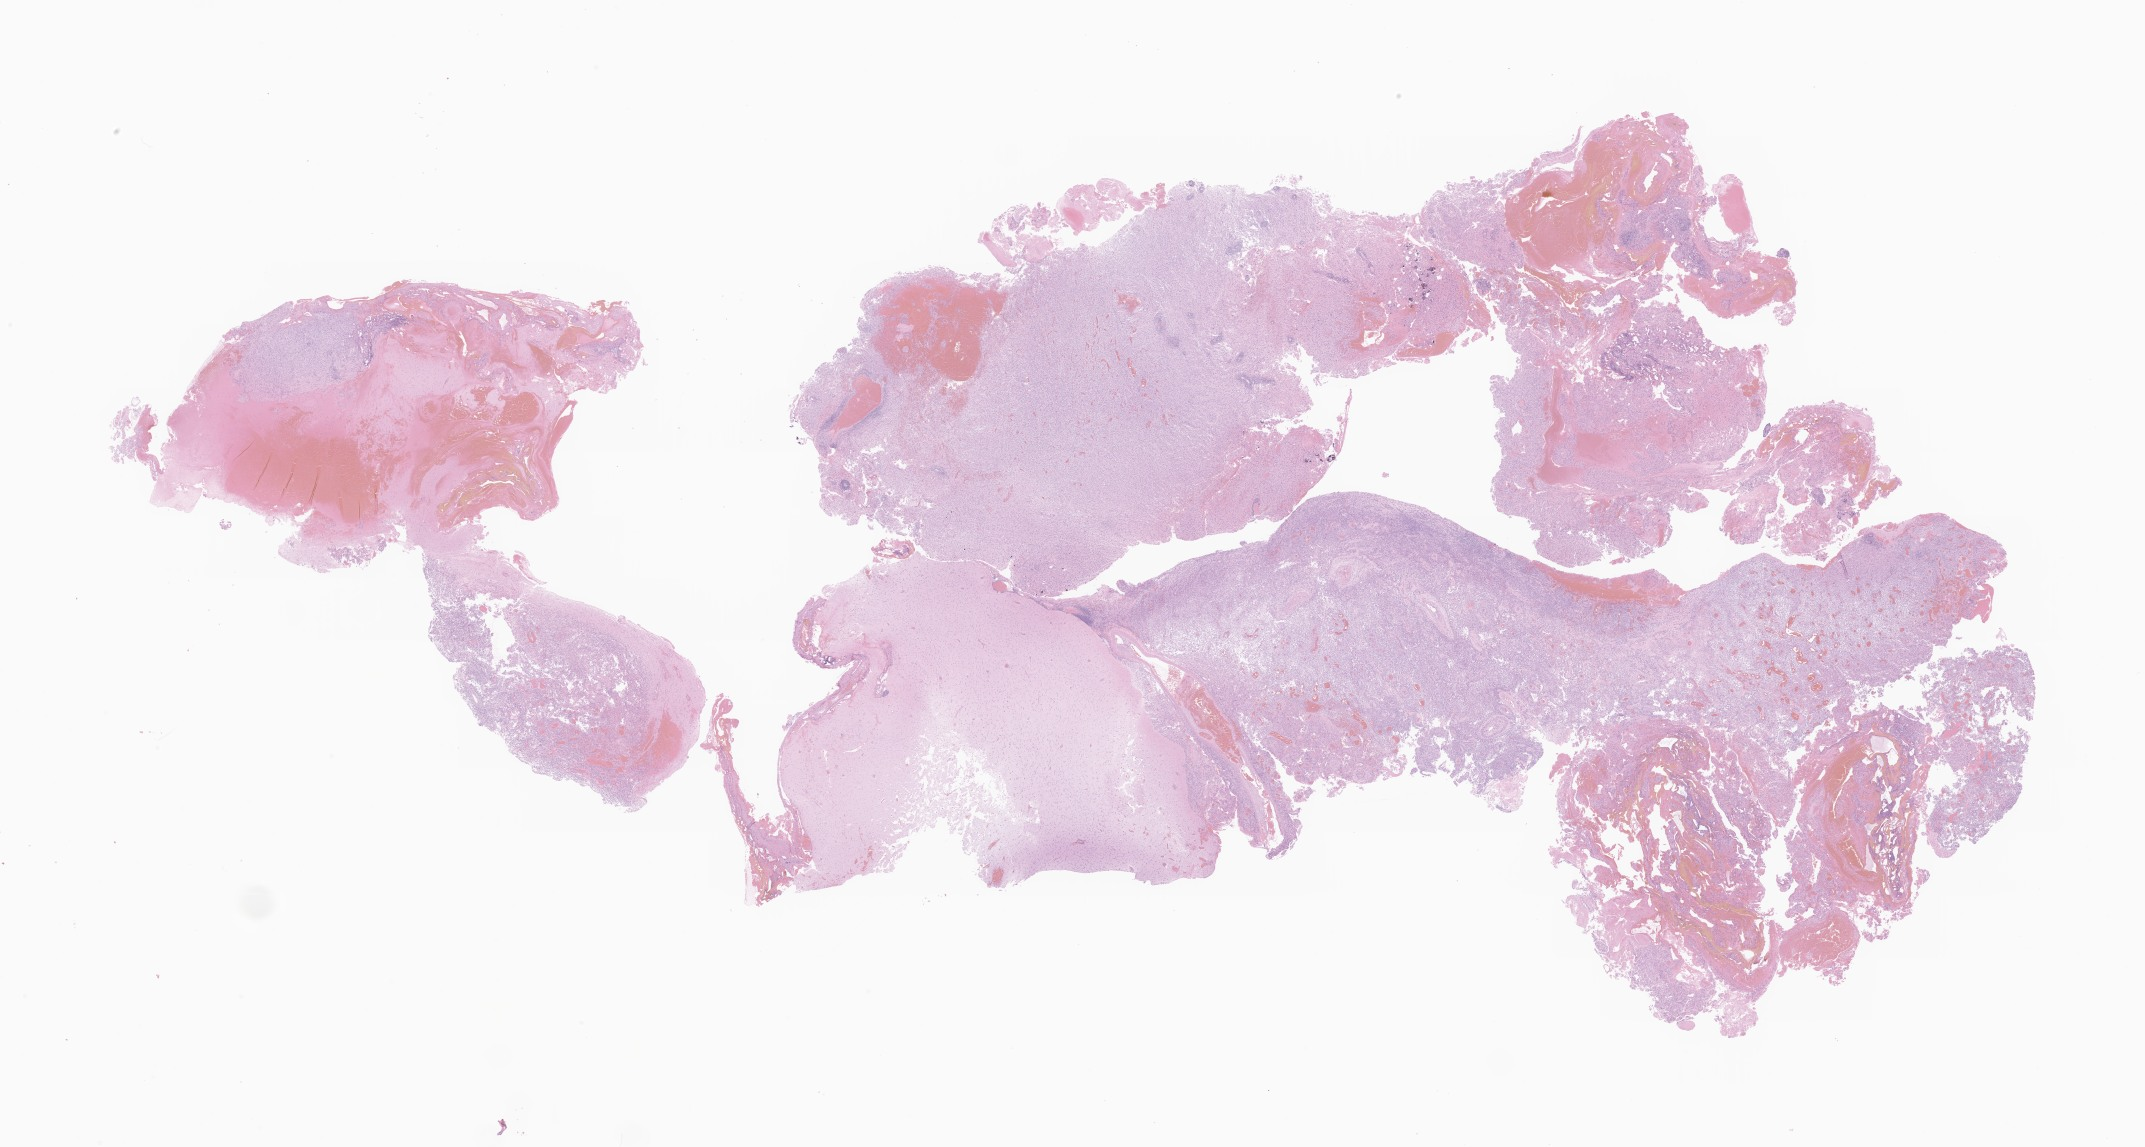
Whole-slide image, haematoxylin and eosin stain of tumor tissue from the brain, low-resolution overview of the scanned area, about 36.2 x 19.3 mm; formalin-fixed, paraffin-embedded (FFPE) tissue. Patient: female, age 221 months (18 years 5 months).
• diagnosis: Neoplasm, malignant